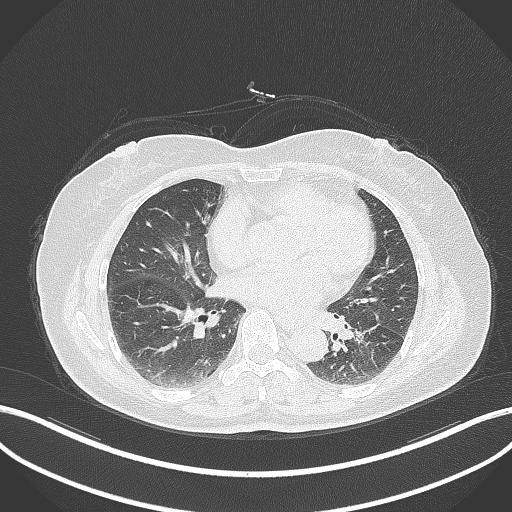
Chest CT, one axial slice. Position 169 of 311 along the scan axis. 120 kVp. Lung window (W 1500 / L -600 HU). 1 mm slice thickness. 512 × 512 image matrix. Female patient, age 59 years. Case-level facts recorded for this patient, not image findings: clinical TNM (as recorded): T2a N0 M0; histopathological grade: G2-3.
Structures marked on this image (bounding box drawn by a radiologist):
- lung tumour (recorded histology: adenocarcinoma): bounding box [x1, y1, x2, y2] px = [351, 323, 383, 367]